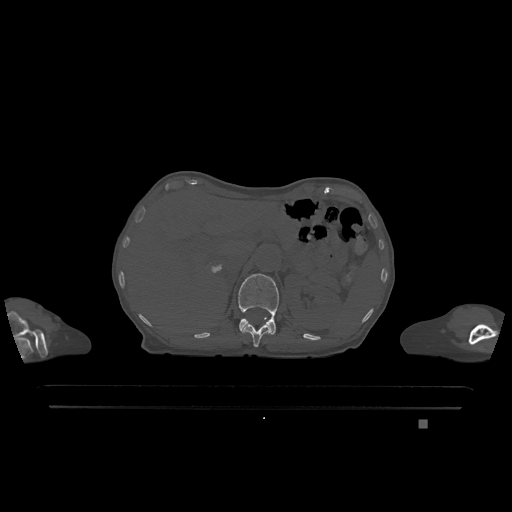
CT including the spine, one axial slice. Bone window (W 1800 / L 400 HU). 512 × 512 image matrix, field of view 500 × 500 mm. Female patient, age 74 years. From the clinical record (not read from this slice): primary cancer: lung; vertebrae with lytic lesions (as recorded): T1, T4, T5, T6, L4, L5.
Structures marked on this image (semi-automatic segmentation, software-assisted and operator-edited):
- L1 vertebra: bounding box (x1, y1, x2, y2) in pixels: (238, 273, 279, 335)
- T12 vertebra: (241, 318, 270, 347)